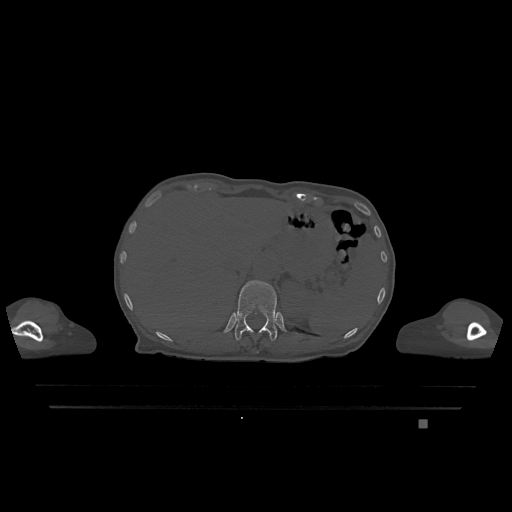
CT including the spine, one axial slice. Slice 543 of 1317 in the series (ordered by position). Bone window (W 1800 / L 400 HU). 512 × 512 image matrix. Patient: female, 74 years. From the clinical record (not read from this slice): primary cancer: lung; vertebrae with lytic lesions (as recorded): T1, T4, T5, T6, L4, L5.
Structures marked on this image (semi-automatically segmented with operator editing):
- T12 vertebra: bounding box <235,281,277,341> (left, top, right, bottom; pixels)